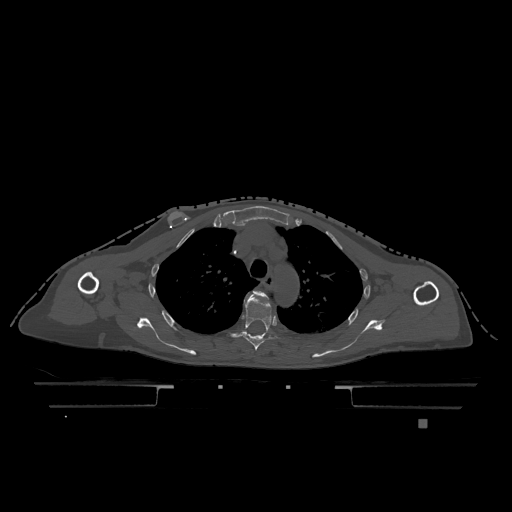
CT including the spine, one axial slice; position 884 of 1317 along the scan axis; bone window (W 1800 / L 400 HU); 512 × 512 image matrix. Female patient, age 74 years. From the clinical record (not read from this slice): primary cancer: lung; vertebrae with lytic lesions (as recorded): T1, T4, T5, T6, L4, L5.
Structures marked on this image (semi-automatically segmented with operator editing):
- T3 vertebra: bounding box (x1, y1, x2, y2) in pixels: (247, 291, 268, 299)
- T4 vertebra: (229, 293, 285, 351)